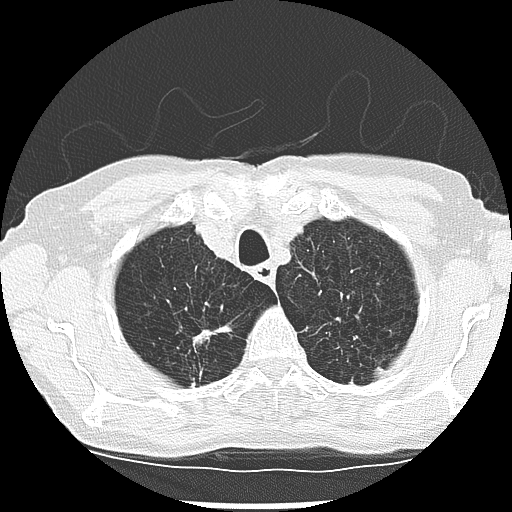
Low-dose screening chest CT, one axial slice. Slice 232 of 265 in the series (ordered by position). Reconstruction kernel LUNG. Lung window (W 1500 / L -600 HU). 512 × 512 image matrix, field of view 300 × 300 mm.
Outlined on this slice (manually delineated by an expert):
- lesion 2 (tumor, upper lobe of right lung): bounding box <193,330,217,345> (left, top, right, bottom; pixels)